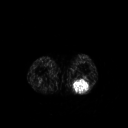
FDG PET of an extremity soft-tissue mass (from a PET/CT study), one axial slice; 128 × 128 image matrix. Male patient, age 54 years. From the clinical record (not read from this slice): histological type: synovial sarcoma; site of the primary tumour: left poplietal fossa.
Structures marked on this image (expert contour drawn on MRI and transferred to this co-registered scan by the dataset authors):
- gross tumour volume (mass): bounding box [x1, y1, x2, y2] px = [72, 78, 91, 93]